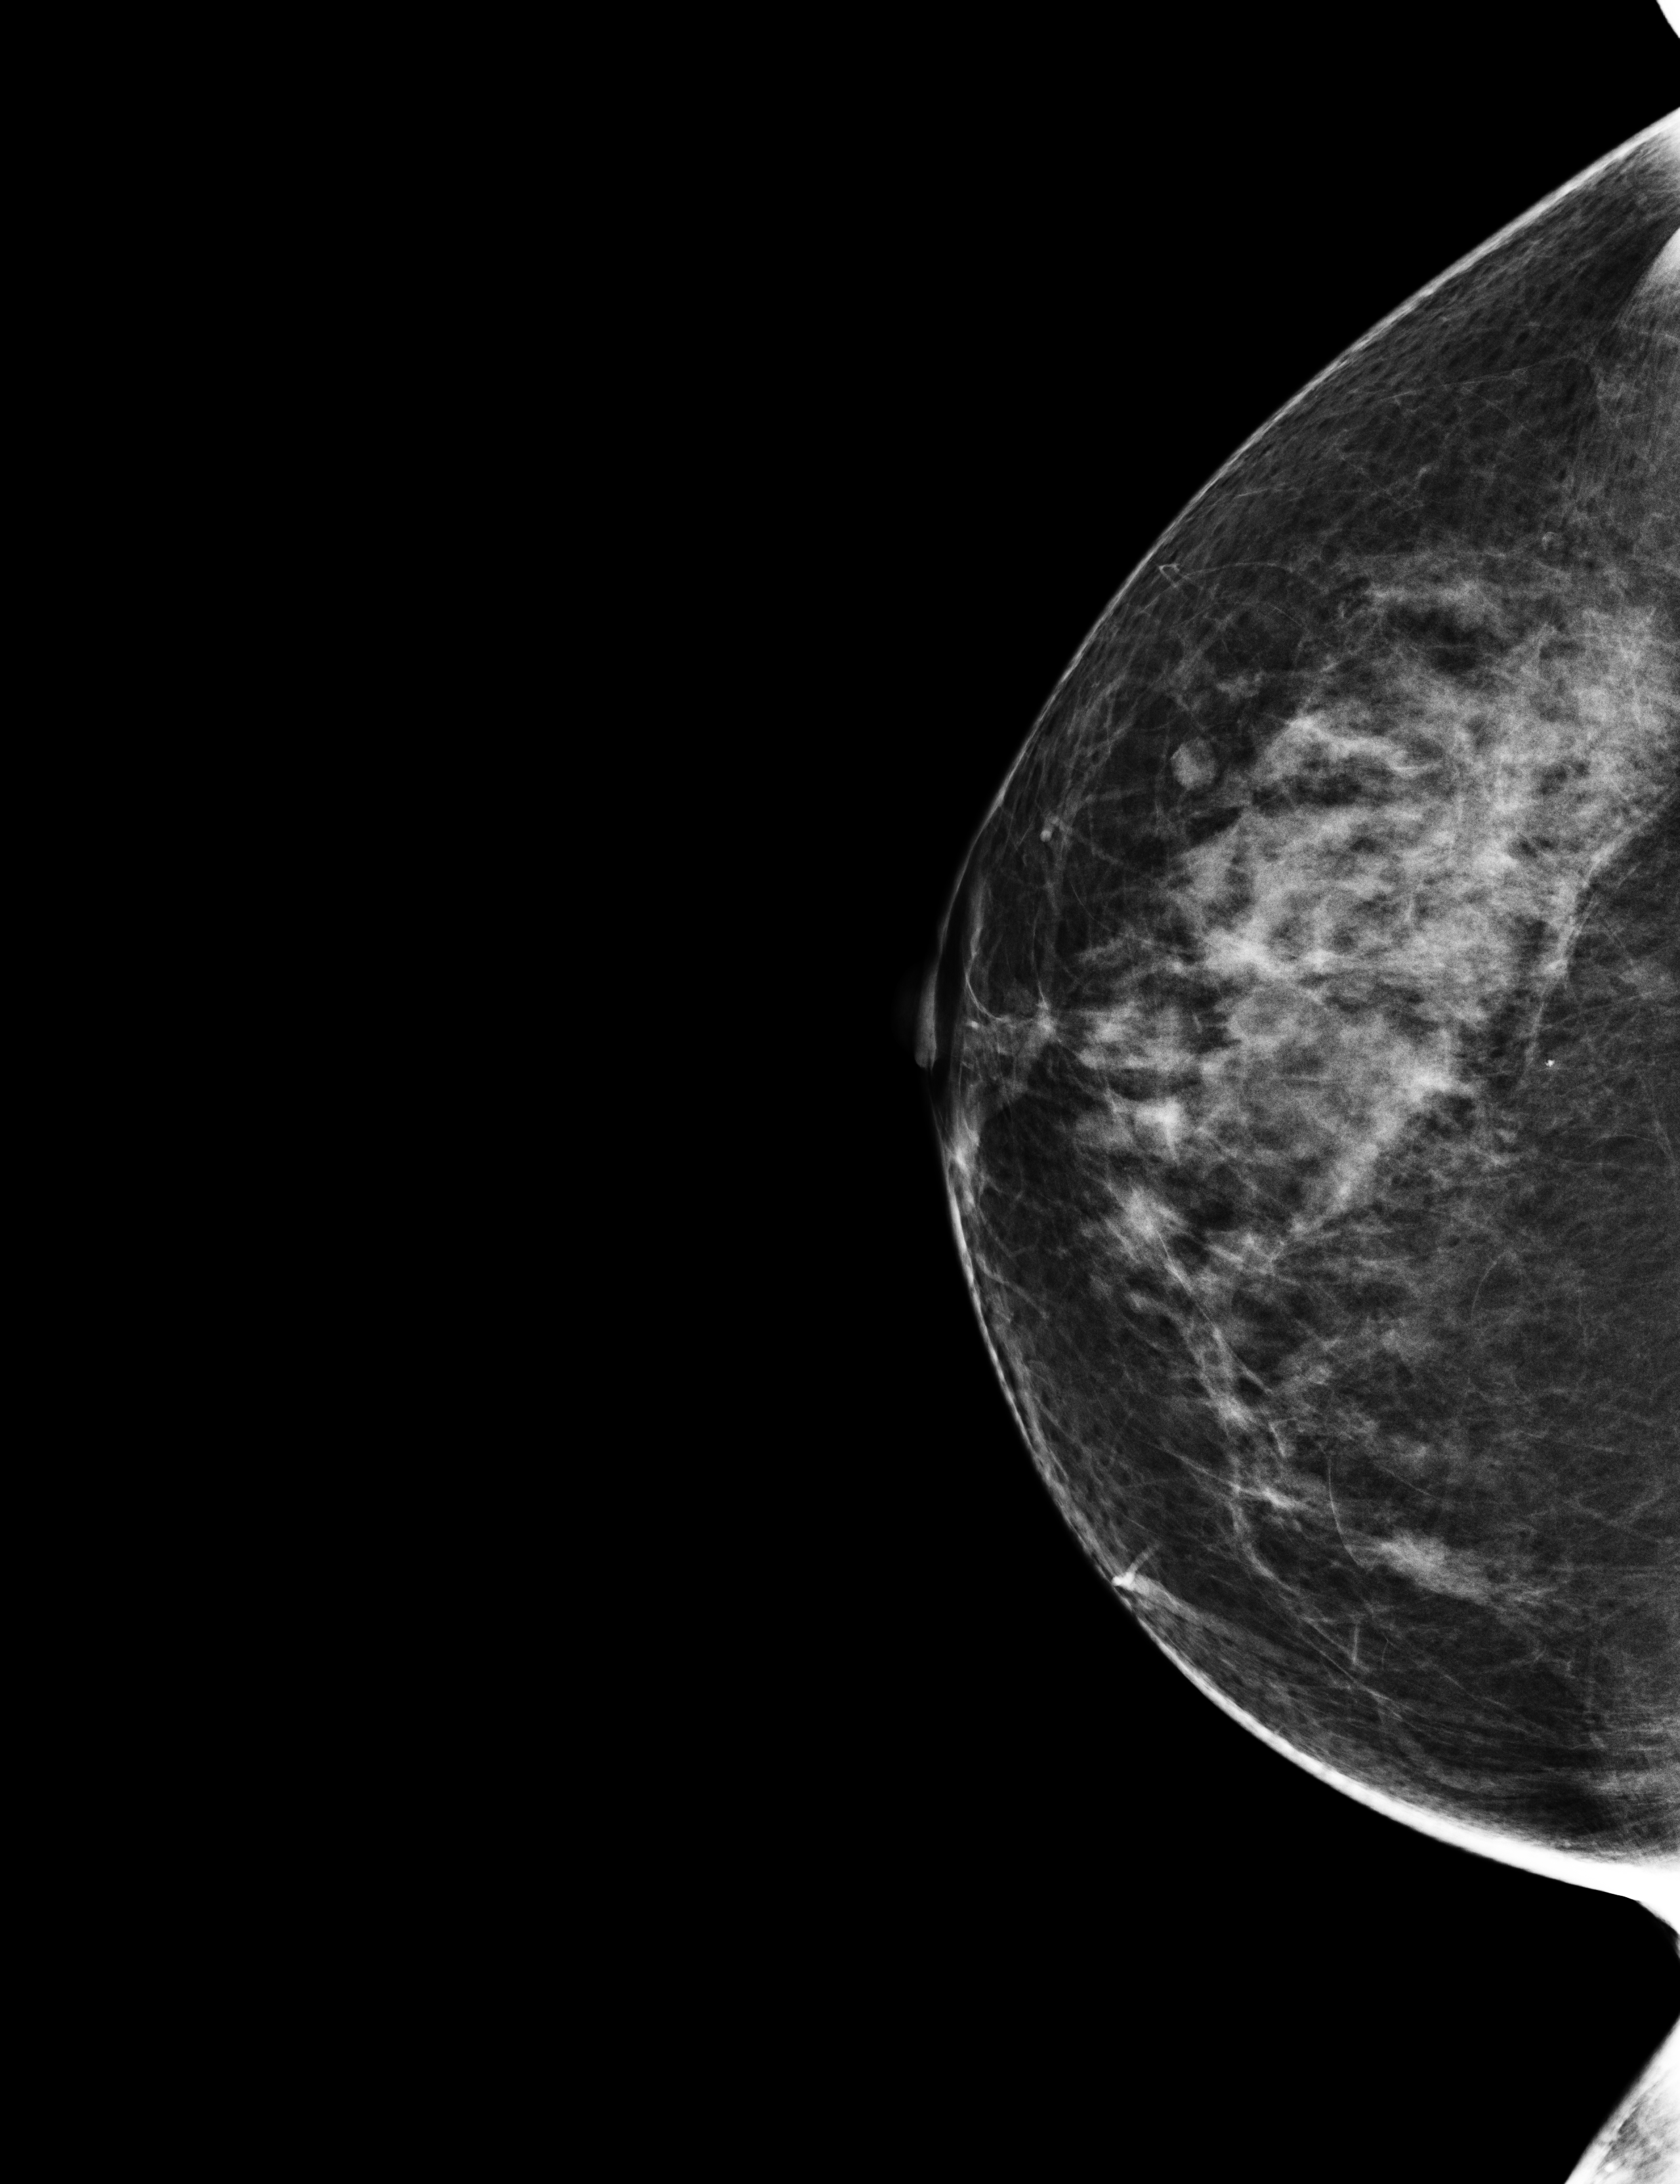
Screening examination; compressed breast thickness 59 mm. Patient aged 55 years (female).
Image type: full-field digital mammogram. Breast: right. Projection: cranio-caudal projection.